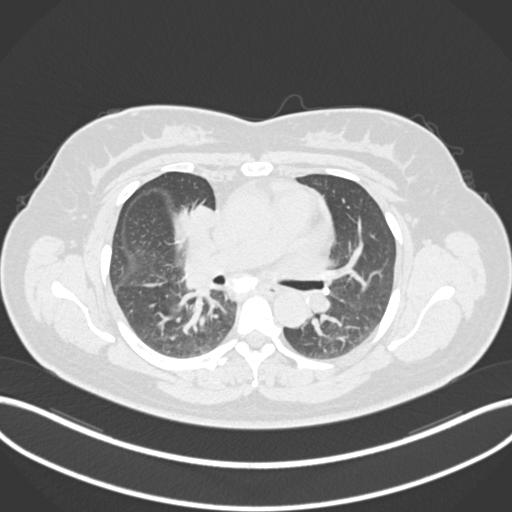
Chest CT, one axial slice. 120 kVp. Lung window (W 1500 / L -600 HU). 1 mm slice thickness. 512 × 512 image matrix, field of view 400 × 400 mm. Female patient, age 46 years. From the clinical record (not read from this slice): clinical TNM (as recorded): T2a N1 M0.
Structures marked on this image (bounding box drawn by a radiologist):
- lung tumour (recorded histology: adenocarcinoma): bounding box (x1, y1, x2, y2) in pixels: (176, 200, 226, 231)